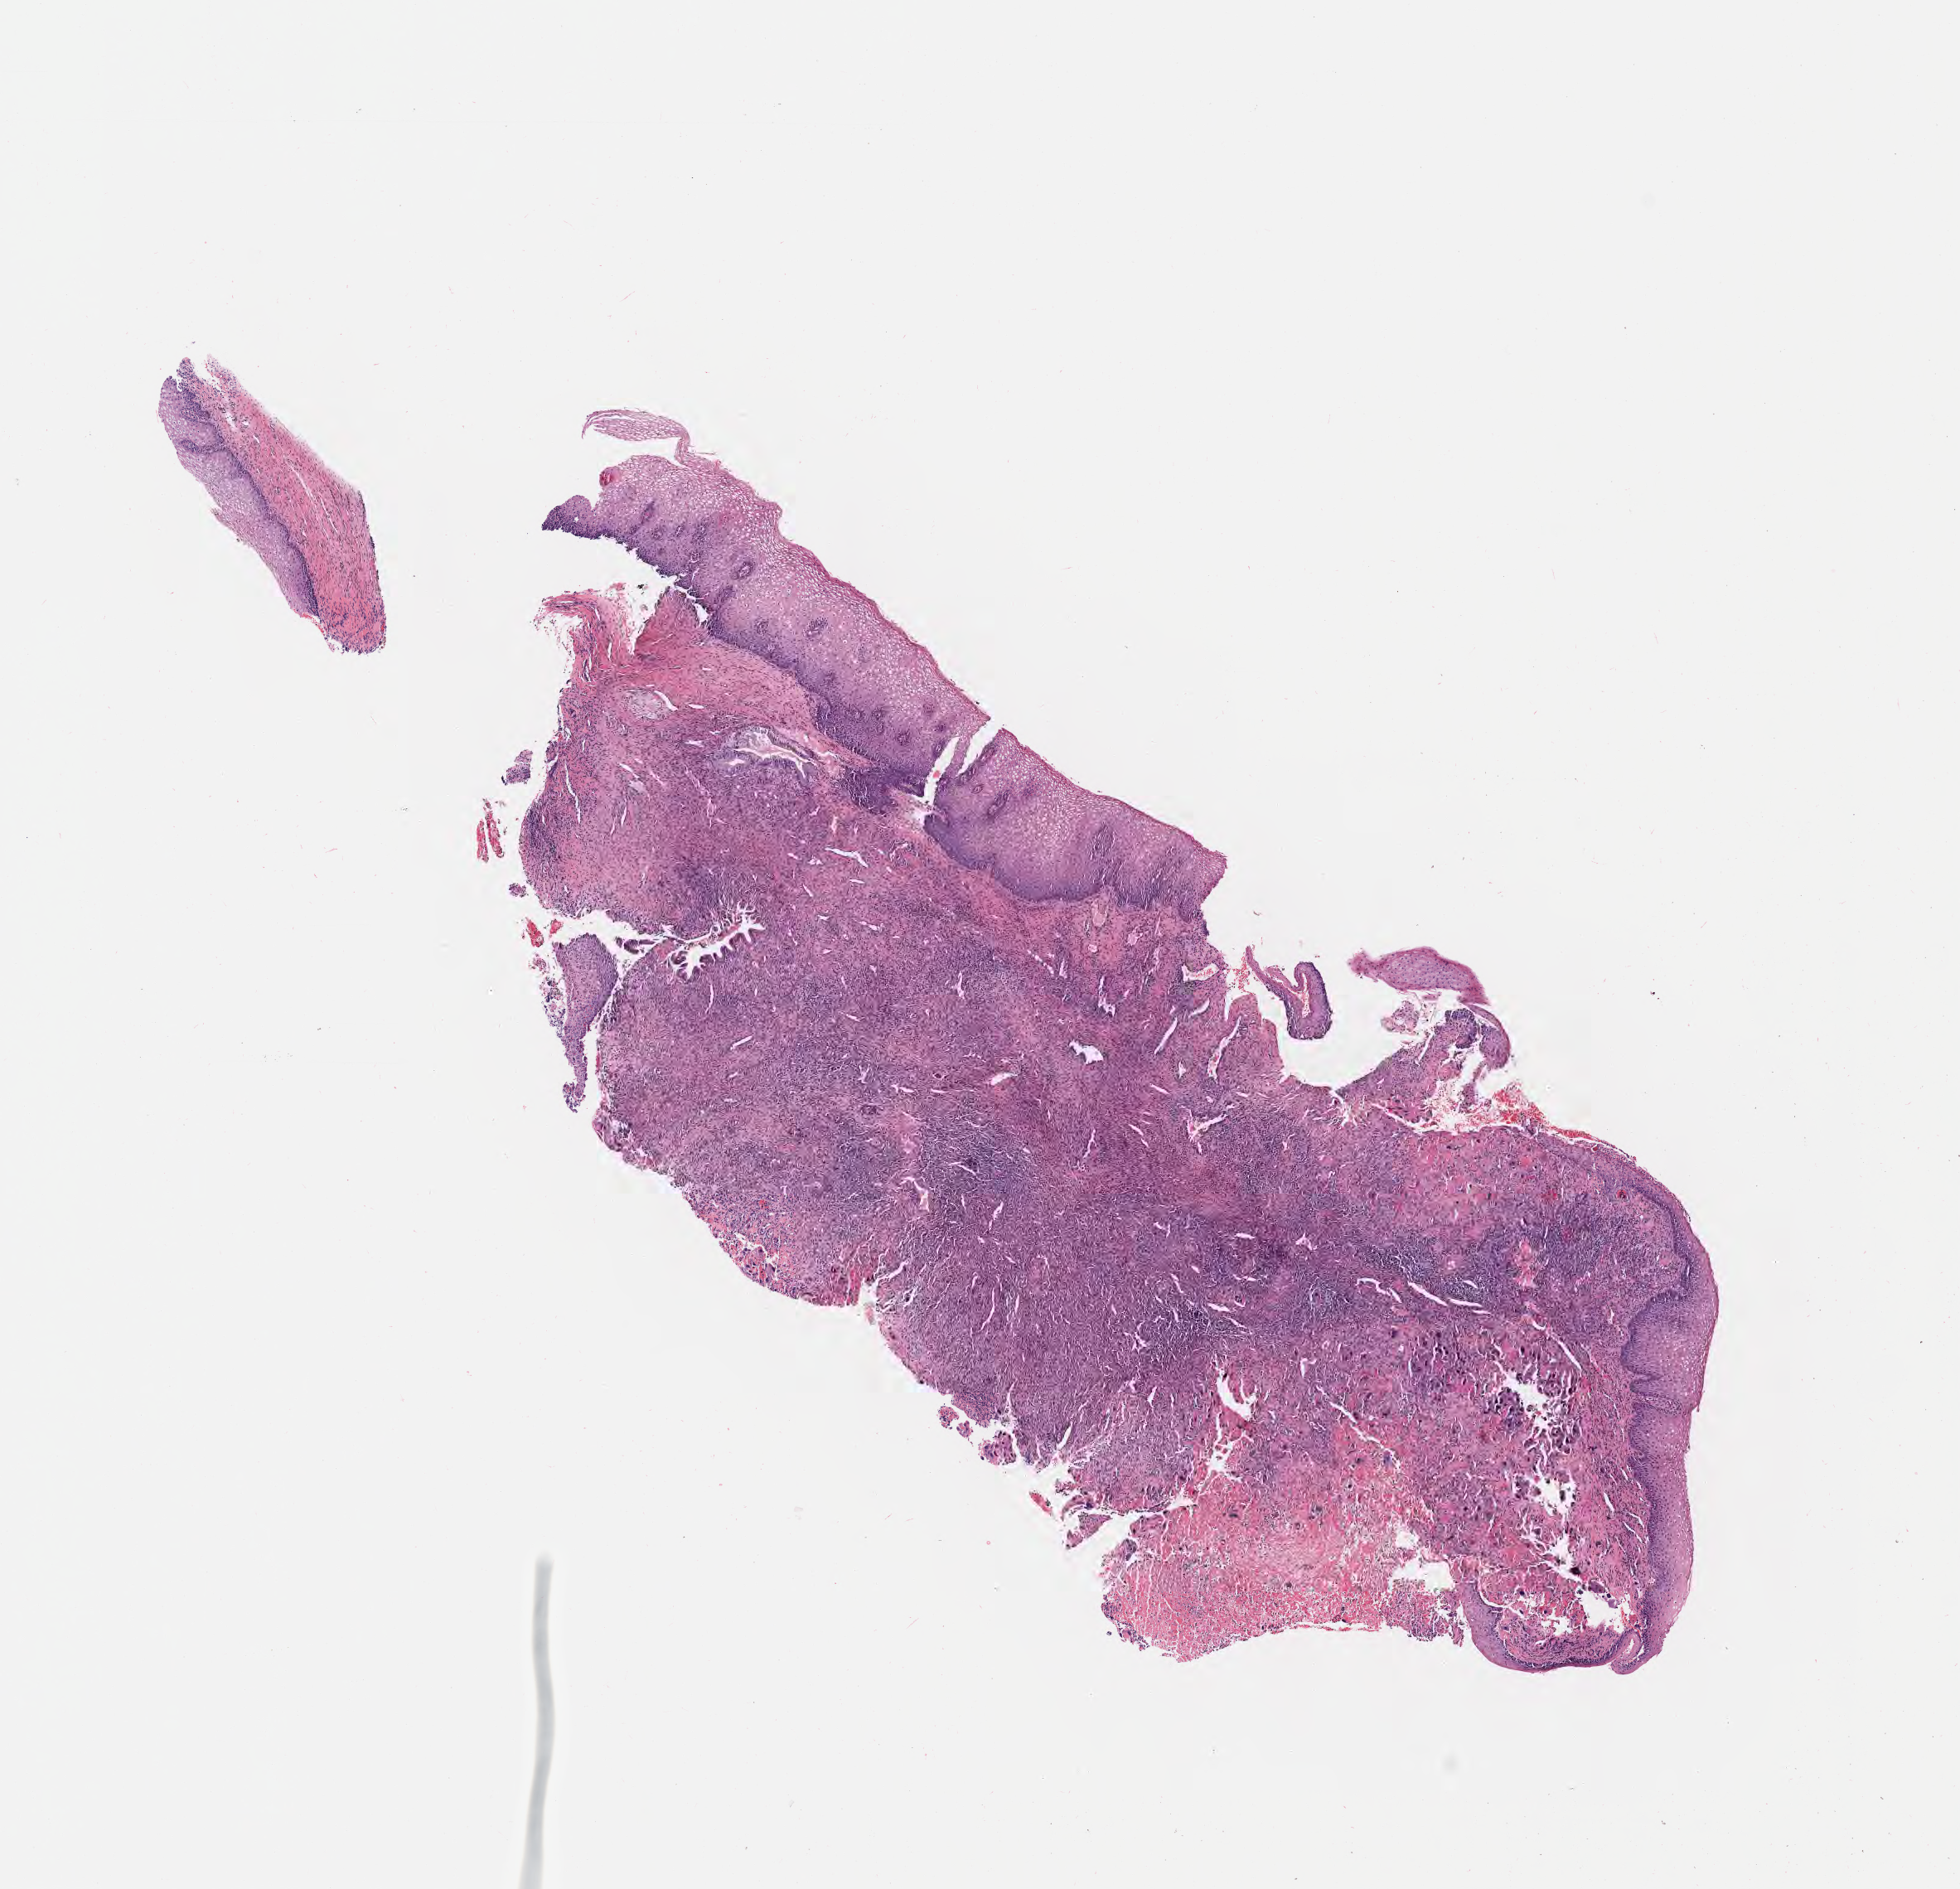
Whole-slide image, hematoxylin and eosin (H&E) stain — shown as a low-resolution overview of the whole scanned area (about 9.6 x 9.2 mm); tumor tissue; site: cervix. Patient: female, aged 46.
* histologic diagnosis: Squamous cell carcinoma, large cell, nonkeratinizing, NOS